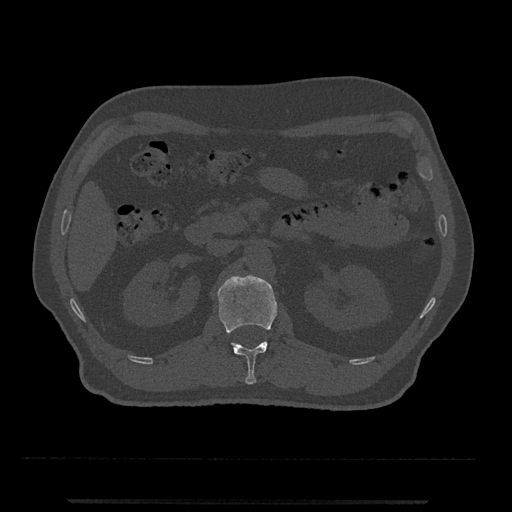
CT including the spine, one axial slice. Slice 323 of 797 in the series (ordered by position). Reconstruction kernel Br40s/3. 120 kVp. Bone window (W 1800 / L 400 HU). 0.5 mm slice thickness. 512 × 512 image matrix, field of view 419 × 419 mm. Patient: male, 63 years. Case-level facts recorded for this patient, not image findings: primary cancer: prostate.
Structures marked on this image (semi-automatically segmented with operator editing):
- L1 vertebra: box from (x=217, y=275) to (x=278, y=385) px